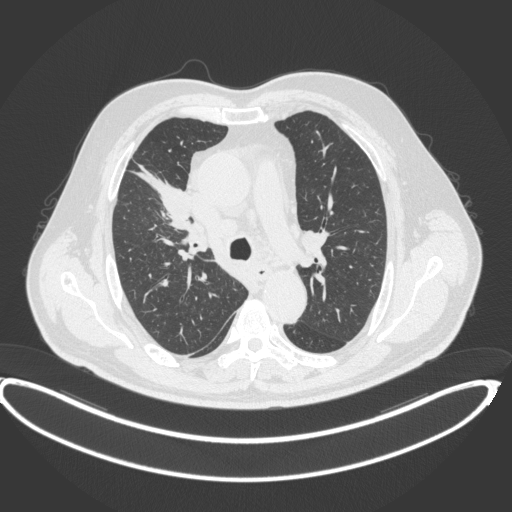
Chest CT, one axial slice. Slice 276 of 395 in the series (ordered by position). Lung window (W 1500 / L -600 HU). 1 mm slice thickness. 512 × 512 image matrix, field of view 448 × 448 mm. Male patient, age 62 years. Case-level facts recorded for this patient, not image findings: clinical TNM (as recorded): T1c N3 M1c.
Structures marked on this image (rectangle marked by the reading radiologist):
- lung tumour (recorded histology: adenocarcinoma): bounding box [x1, y1, x2, y2] px = [131, 160, 191, 235]